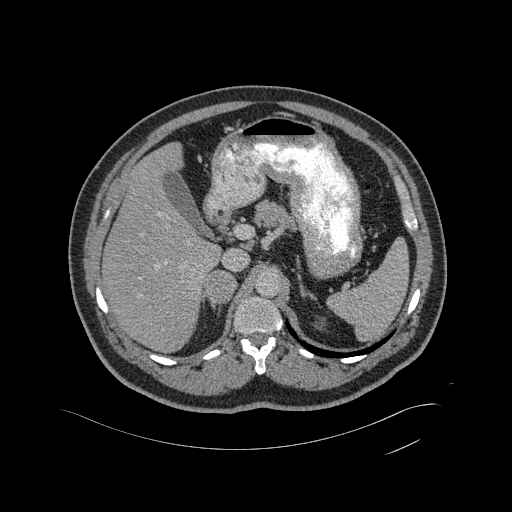
Contrast-enhanced abdominal CT, one axial slice; position 321 of 433 along the scan axis; intravenous contrast given; soft-tissue window (W 400 / L 40 HU); 2 mm slice thickness; 512 × 512 image matrix. Male patient, age 56 years. Case-level facts recorded for this patient, not image findings: diagnosis: adrenocortical carcinoma; tumour side: right adrenal; tumour size at pathology: 11.6 cm; Ki-67 index: 50 %; stage (as recorded): 3.
Structures marked on this image (semi-automatically segmented with operator editing):
- mass: bounding box <206,271,235,302> (left, top, right, bottom; pixels)